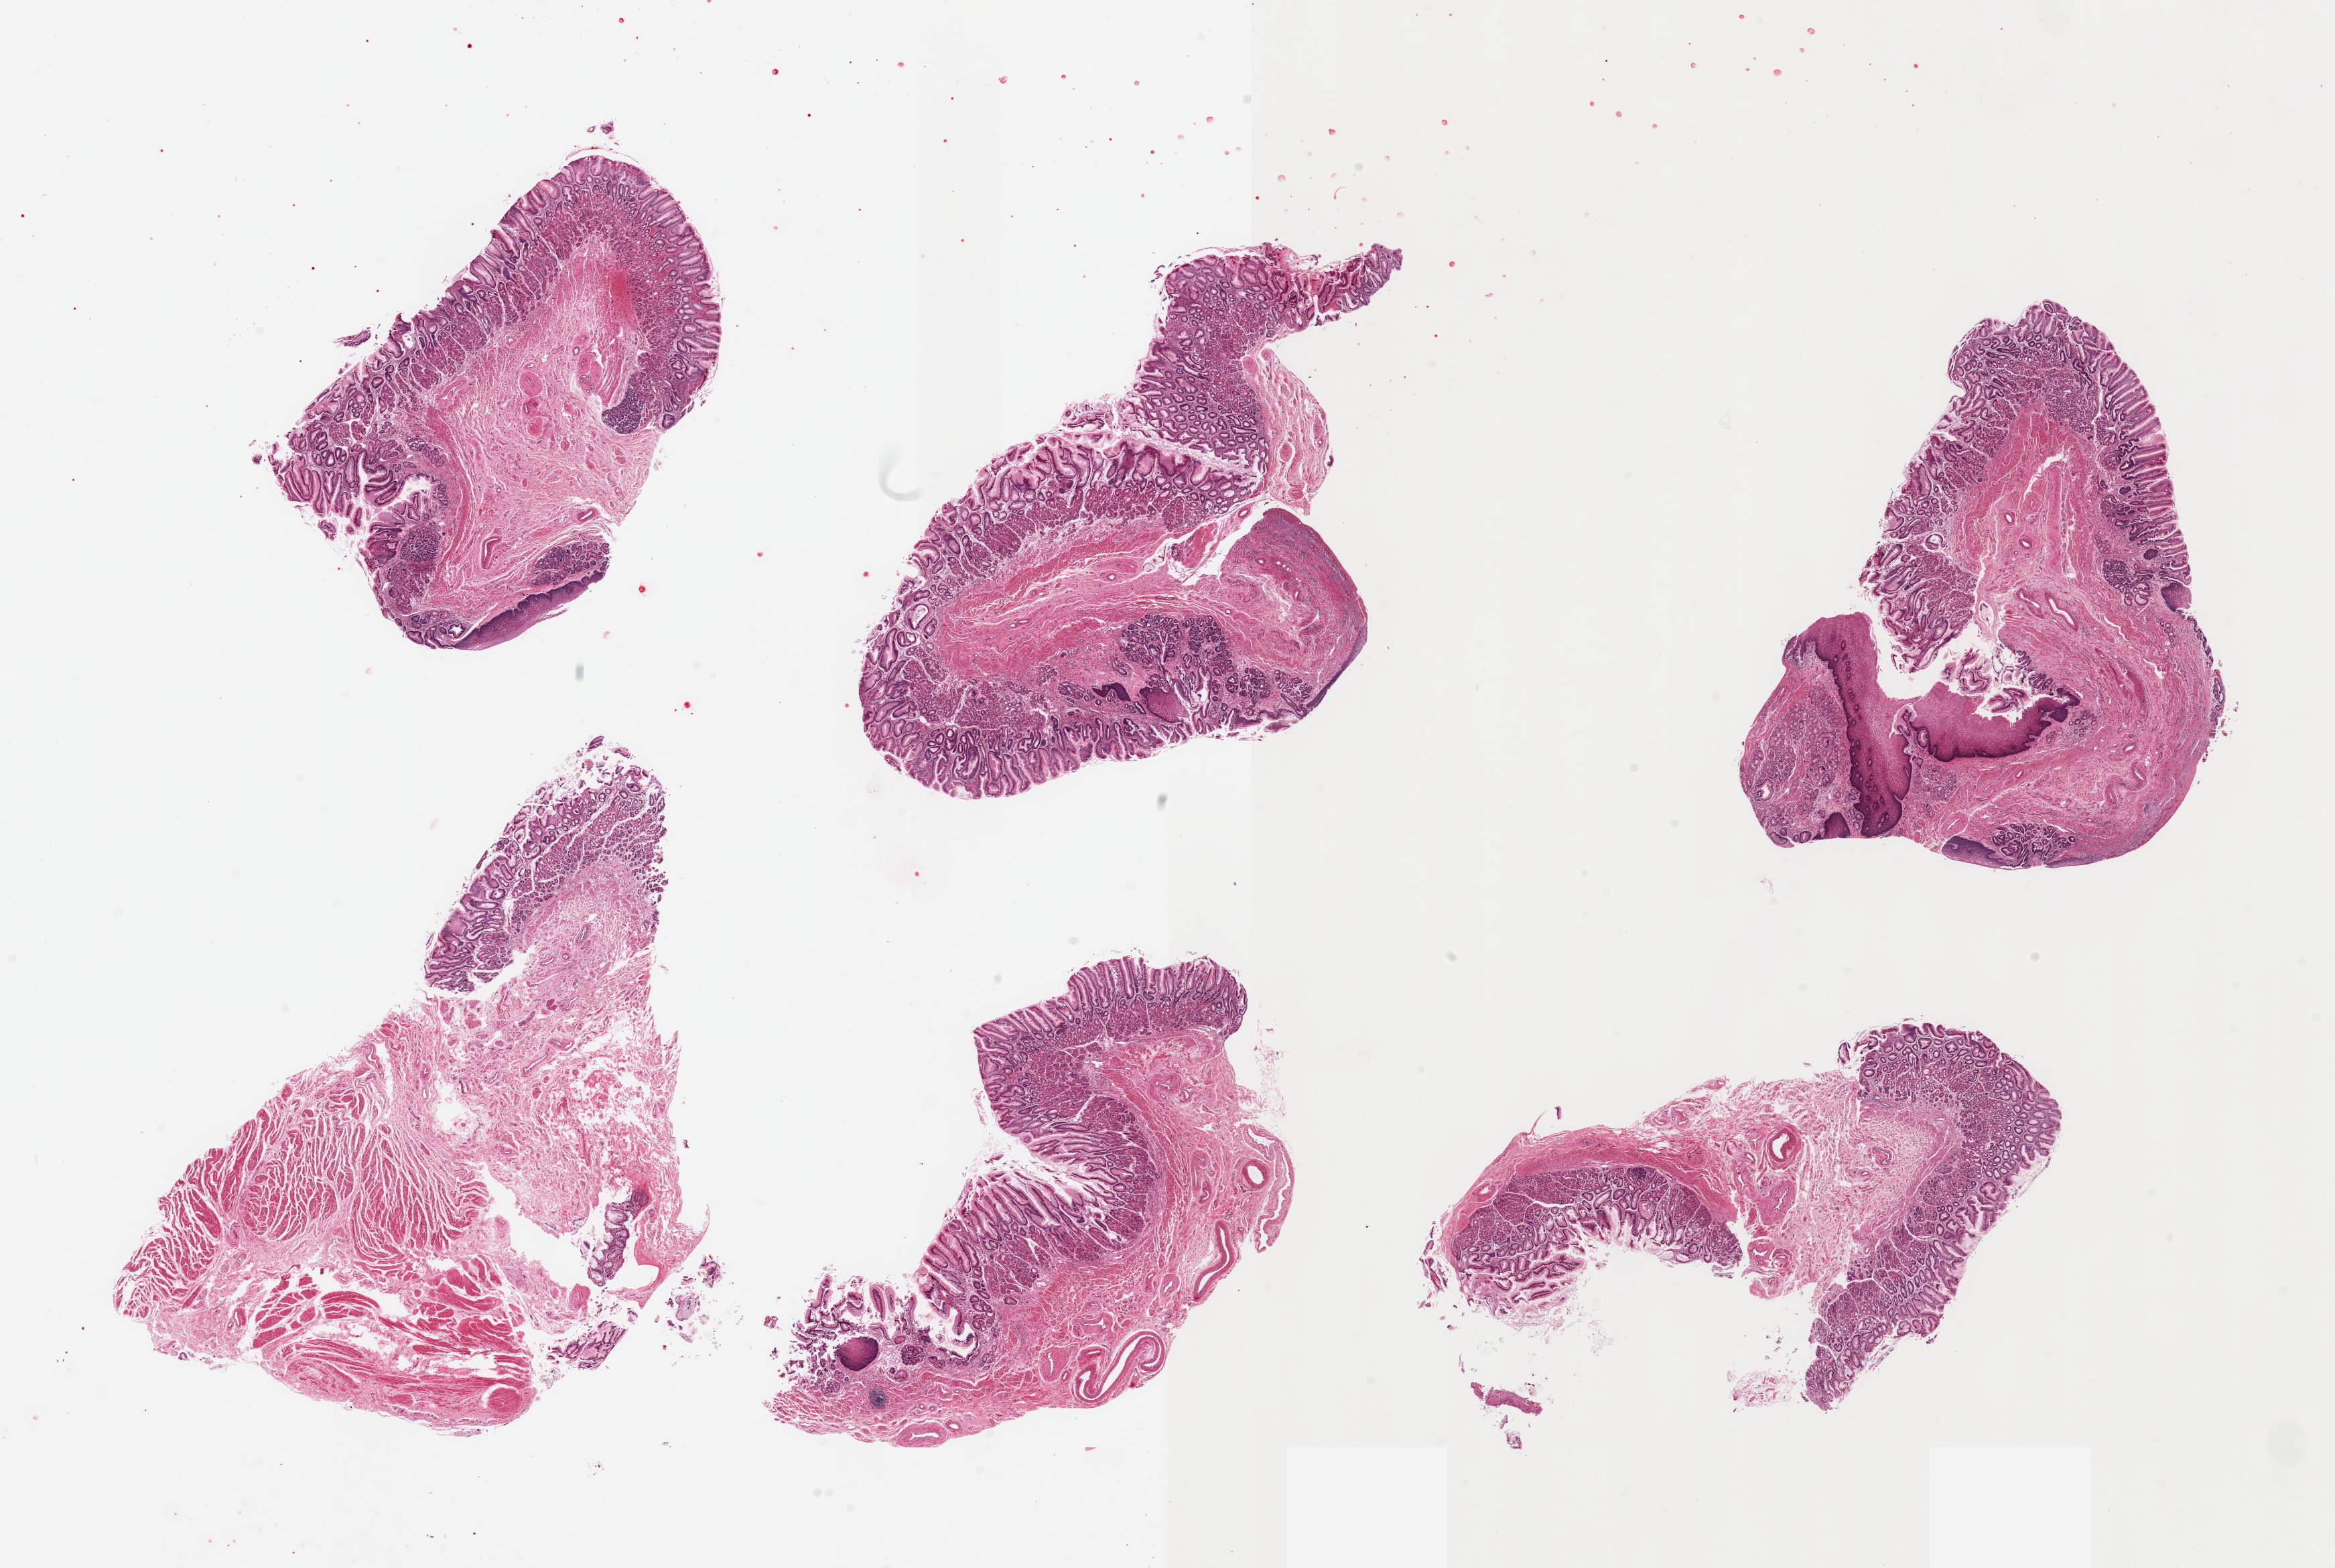
Whole-slide image, haematoxylin and eosin stain, shown as a low-resolution overview of the whole scanned area (about 27.6 x 18.5 mm, acquisition: 20x scan); PAXgene-fixed paraffin-embedded (PFPE) section; section of gastroesophageal junction (target tissue); tissue donor sample.
* review note (as recorded): 6 pieces; non target gastric and esophageal mucosa with lamina propria; insufficient representation of target muscularis